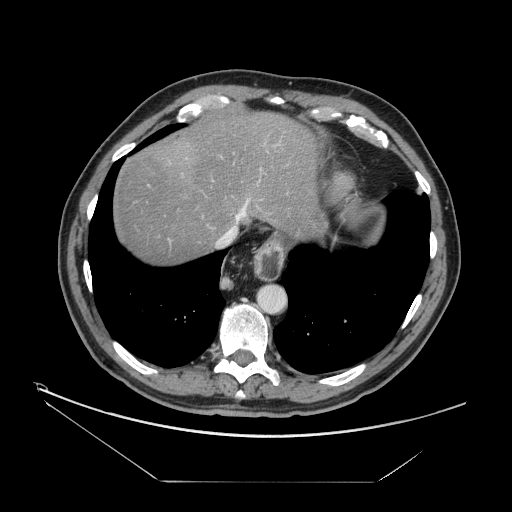
Contrast-enhanced abdominal CT, one axial slice. Reconstruction kernel STANDARD. Intravenous contrast given. Soft-tissue window (W 400 / L 40 HU). 2.5 mm slice thickness. 512 × 512 image matrix, field of view 440 × 440 mm. Male patient, age 65 years. From the clinical record (not read from this slice): diagnosis: colorectal cancer liver metastases, imaged before liver resection; multiple liver metastases: yes.
Structures marked on this image (outlined manually by an expert reader):
- hepatic veins: bounding box <218,199,249,244> (left, top, right, bottom; pixels)
- liver: <112,108,318,263>
- planned liver remnant (the part of the liver to remain after resection): <112,108,318,263>
- portal vein (with intrahepatic branches): <148,158,187,241>